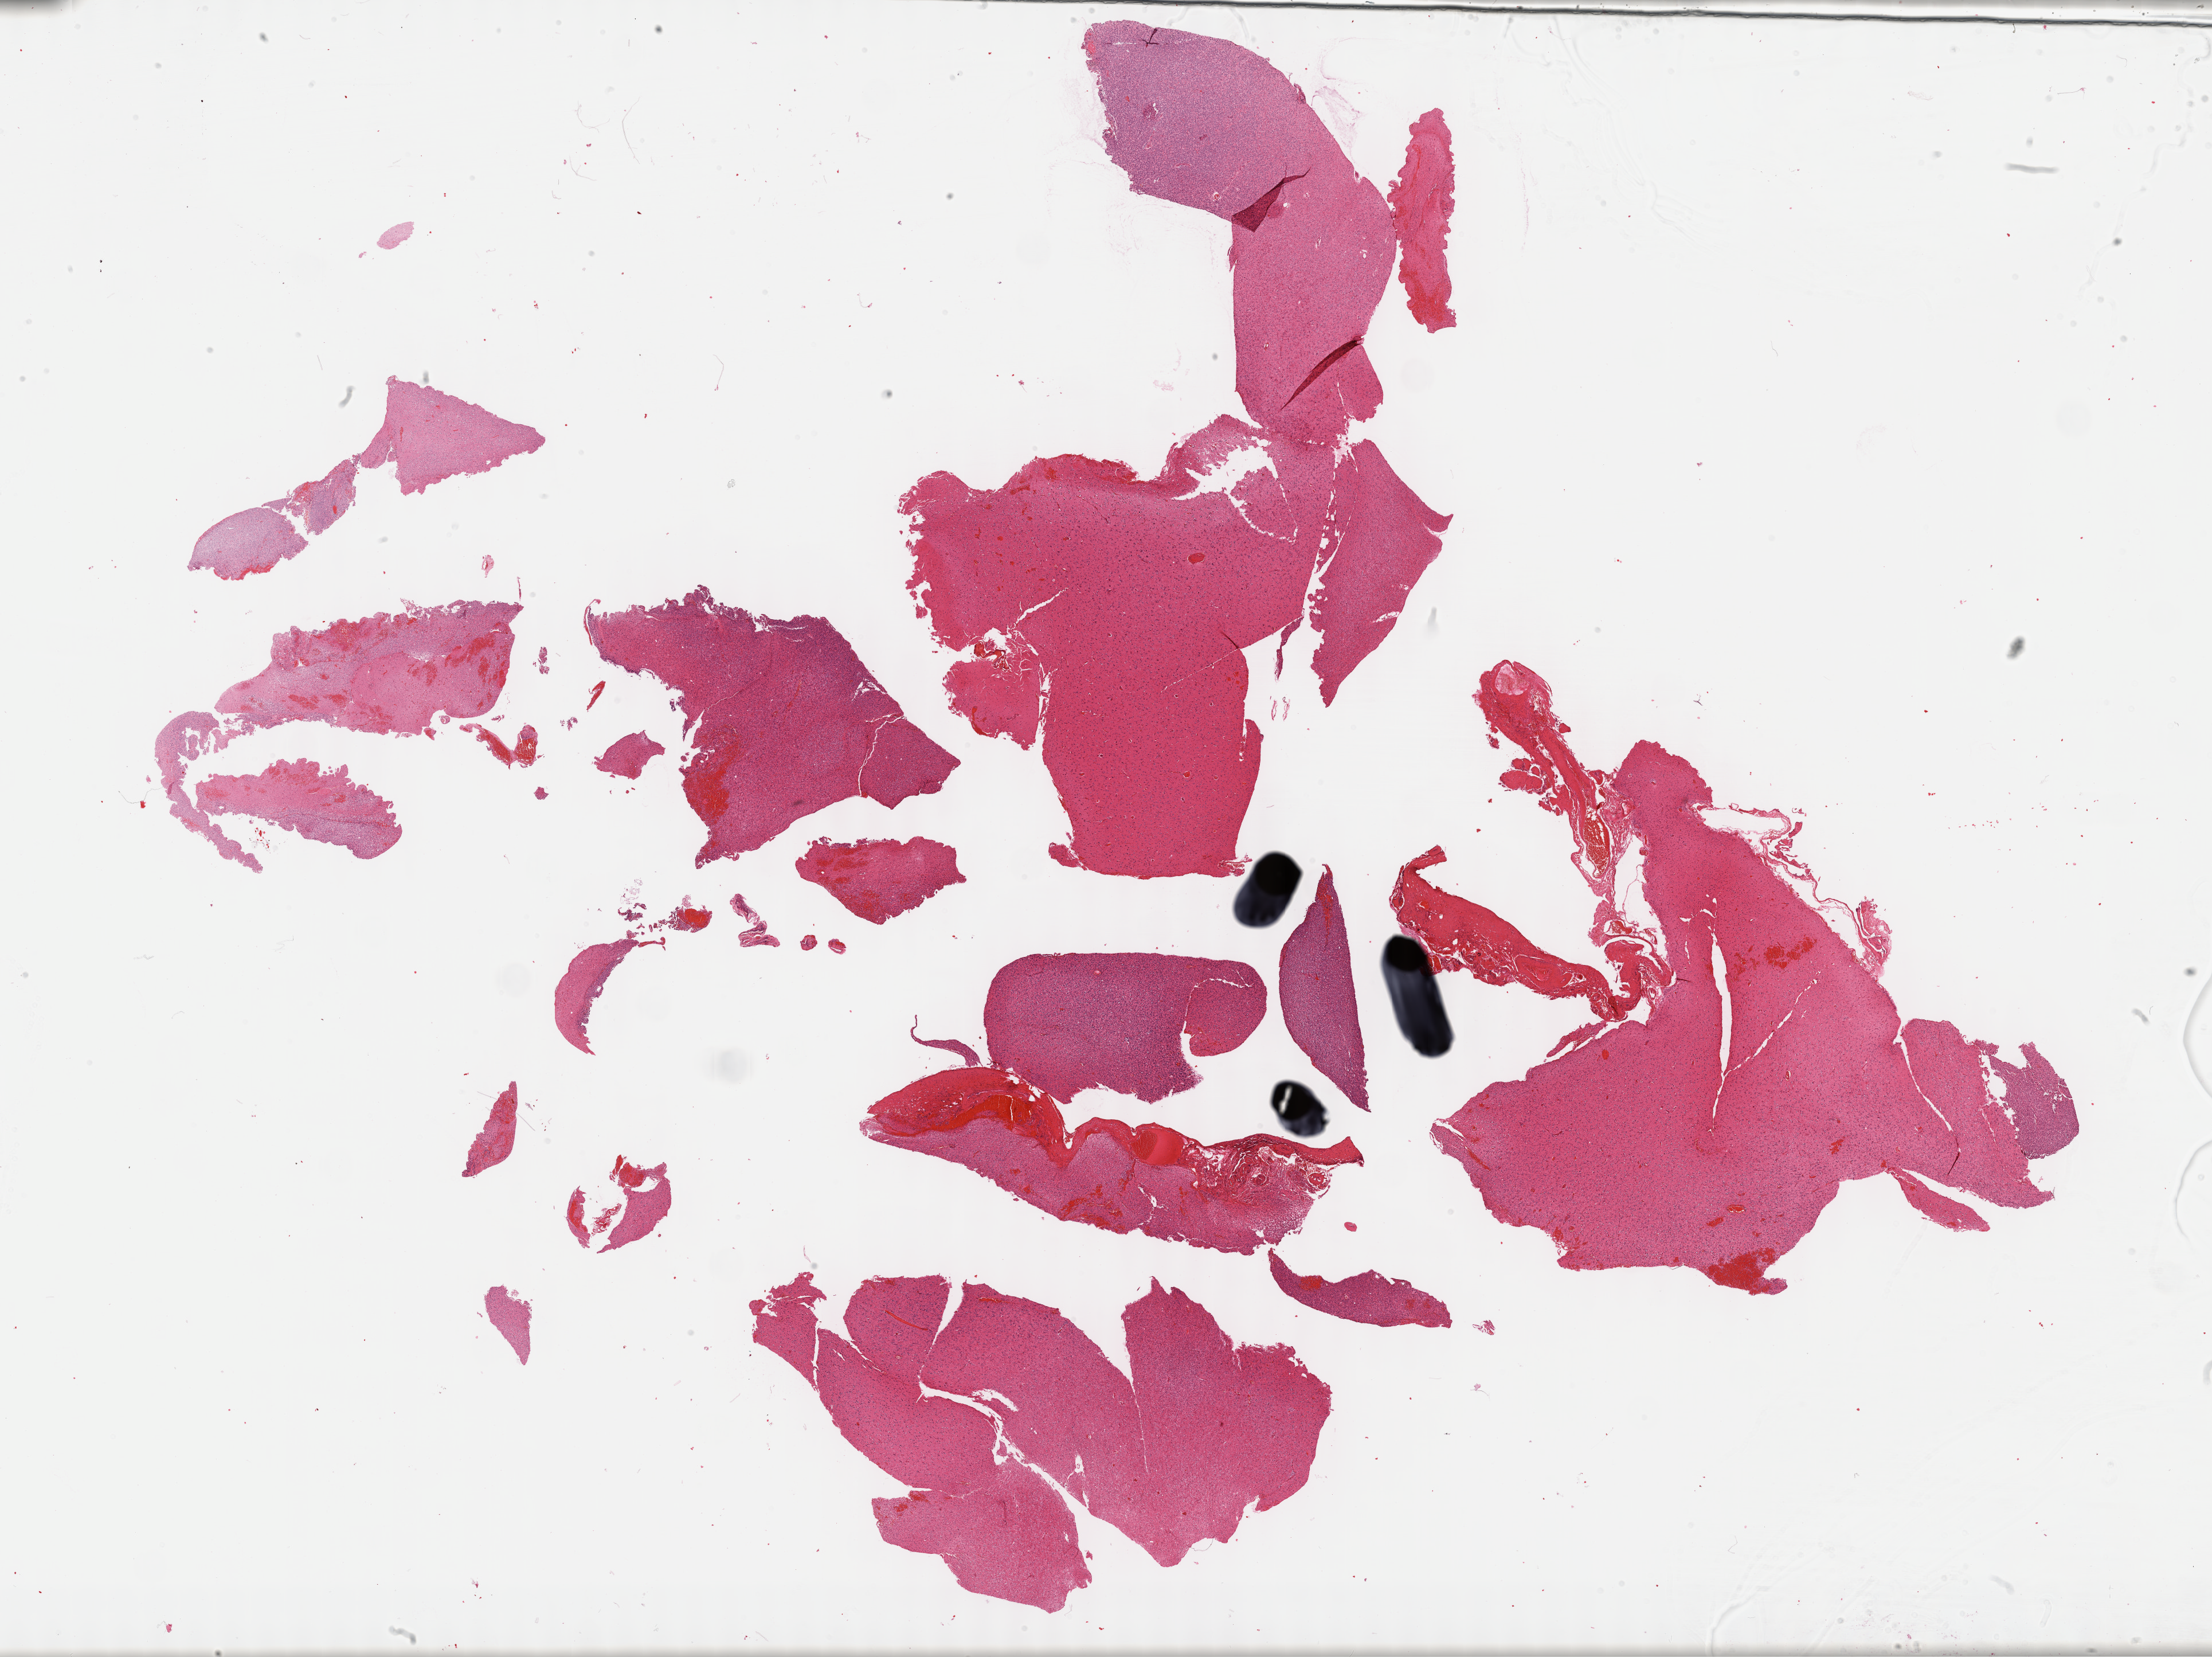
Digitized H&E-stained tissue section (whole slide) — shown as a low-resolution overview of the whole scanned area (about 31.2 x 23.4 mm, slide scanned at 40x). Formalin-fixed paraffin-embedded (FFPE) diagnostic section. Brain, primary tumour sample. Male patient; age at initial diagnosis 41 years. Histologic grade: G2 (moderately differentiated).
* pathologic diagnosis: Oligodendroglioma, NOS (cerebrum)
* laterality: left